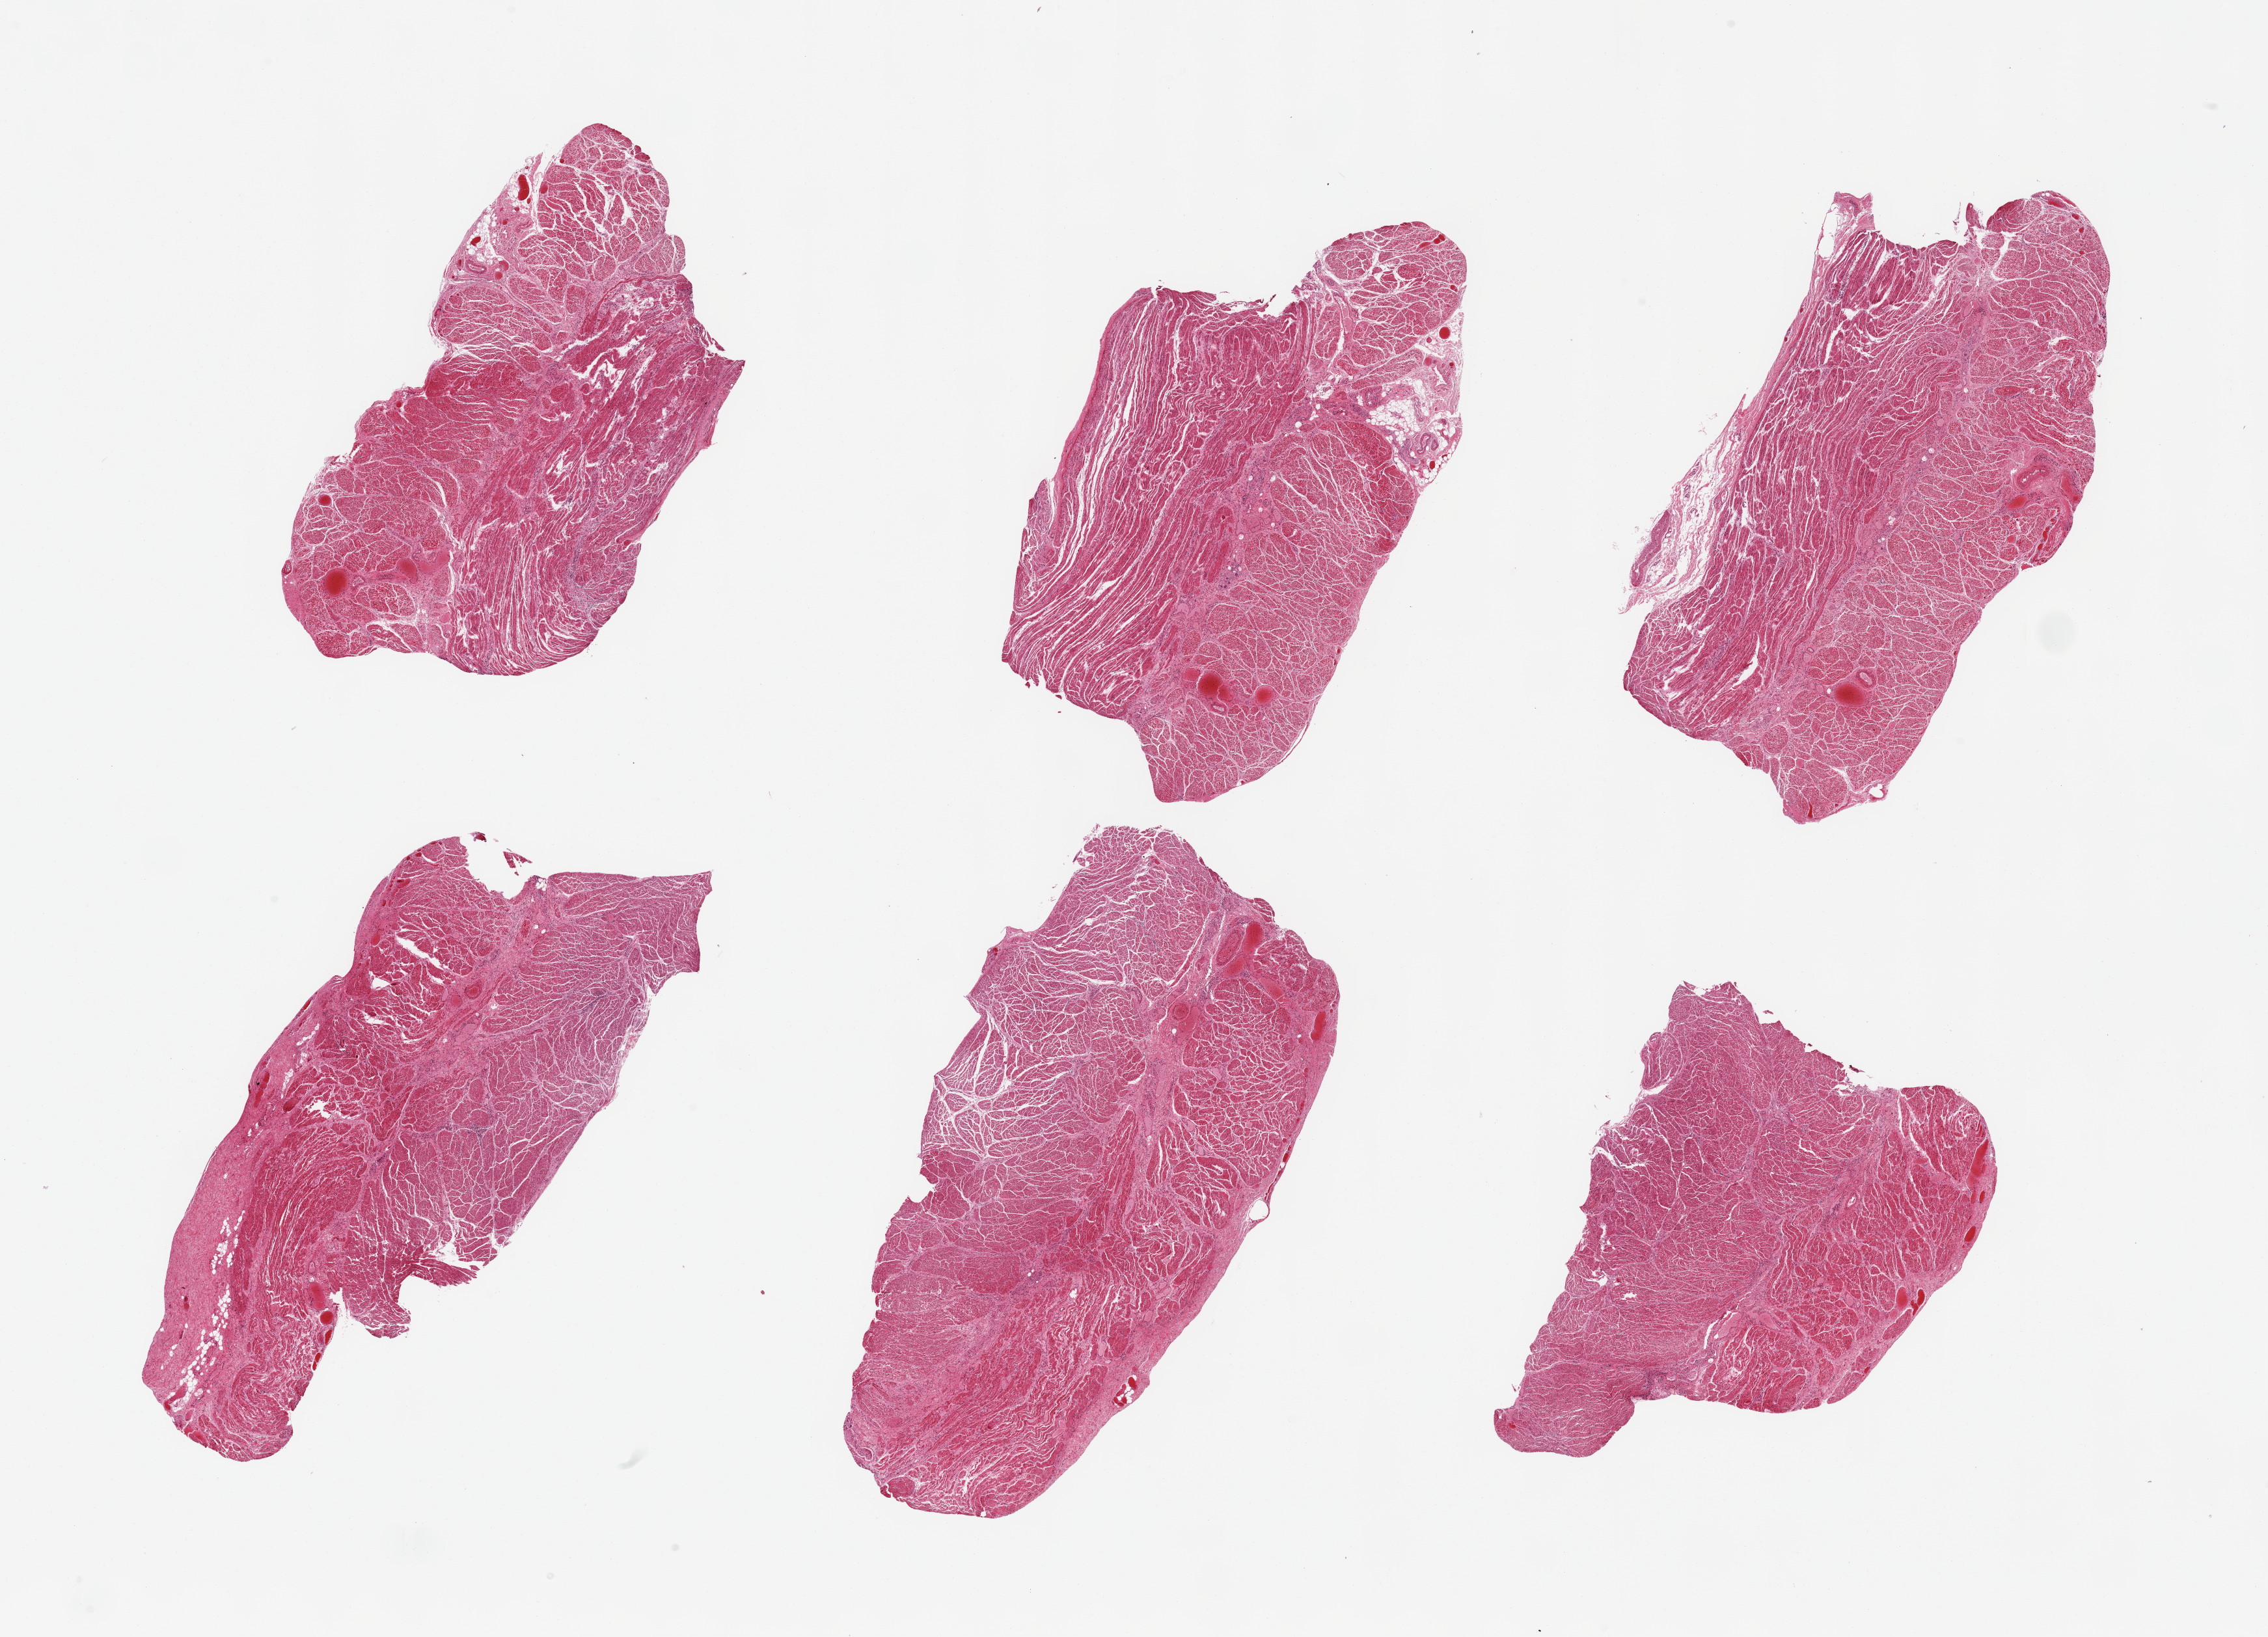
Digitized hematoxylin and eosin (H&E)-stained section, low-resolution overview of the scanned area, about 27.6 x 19.9 mm (slide scanned at 20x); PAXgene-fixed, paraffin-embedded tissue; sampled site (target tissue): esophageal muscle; tissue donor sample. Male donor.
Review note (as recorded): 6 pieces, confirmed target muscularis.